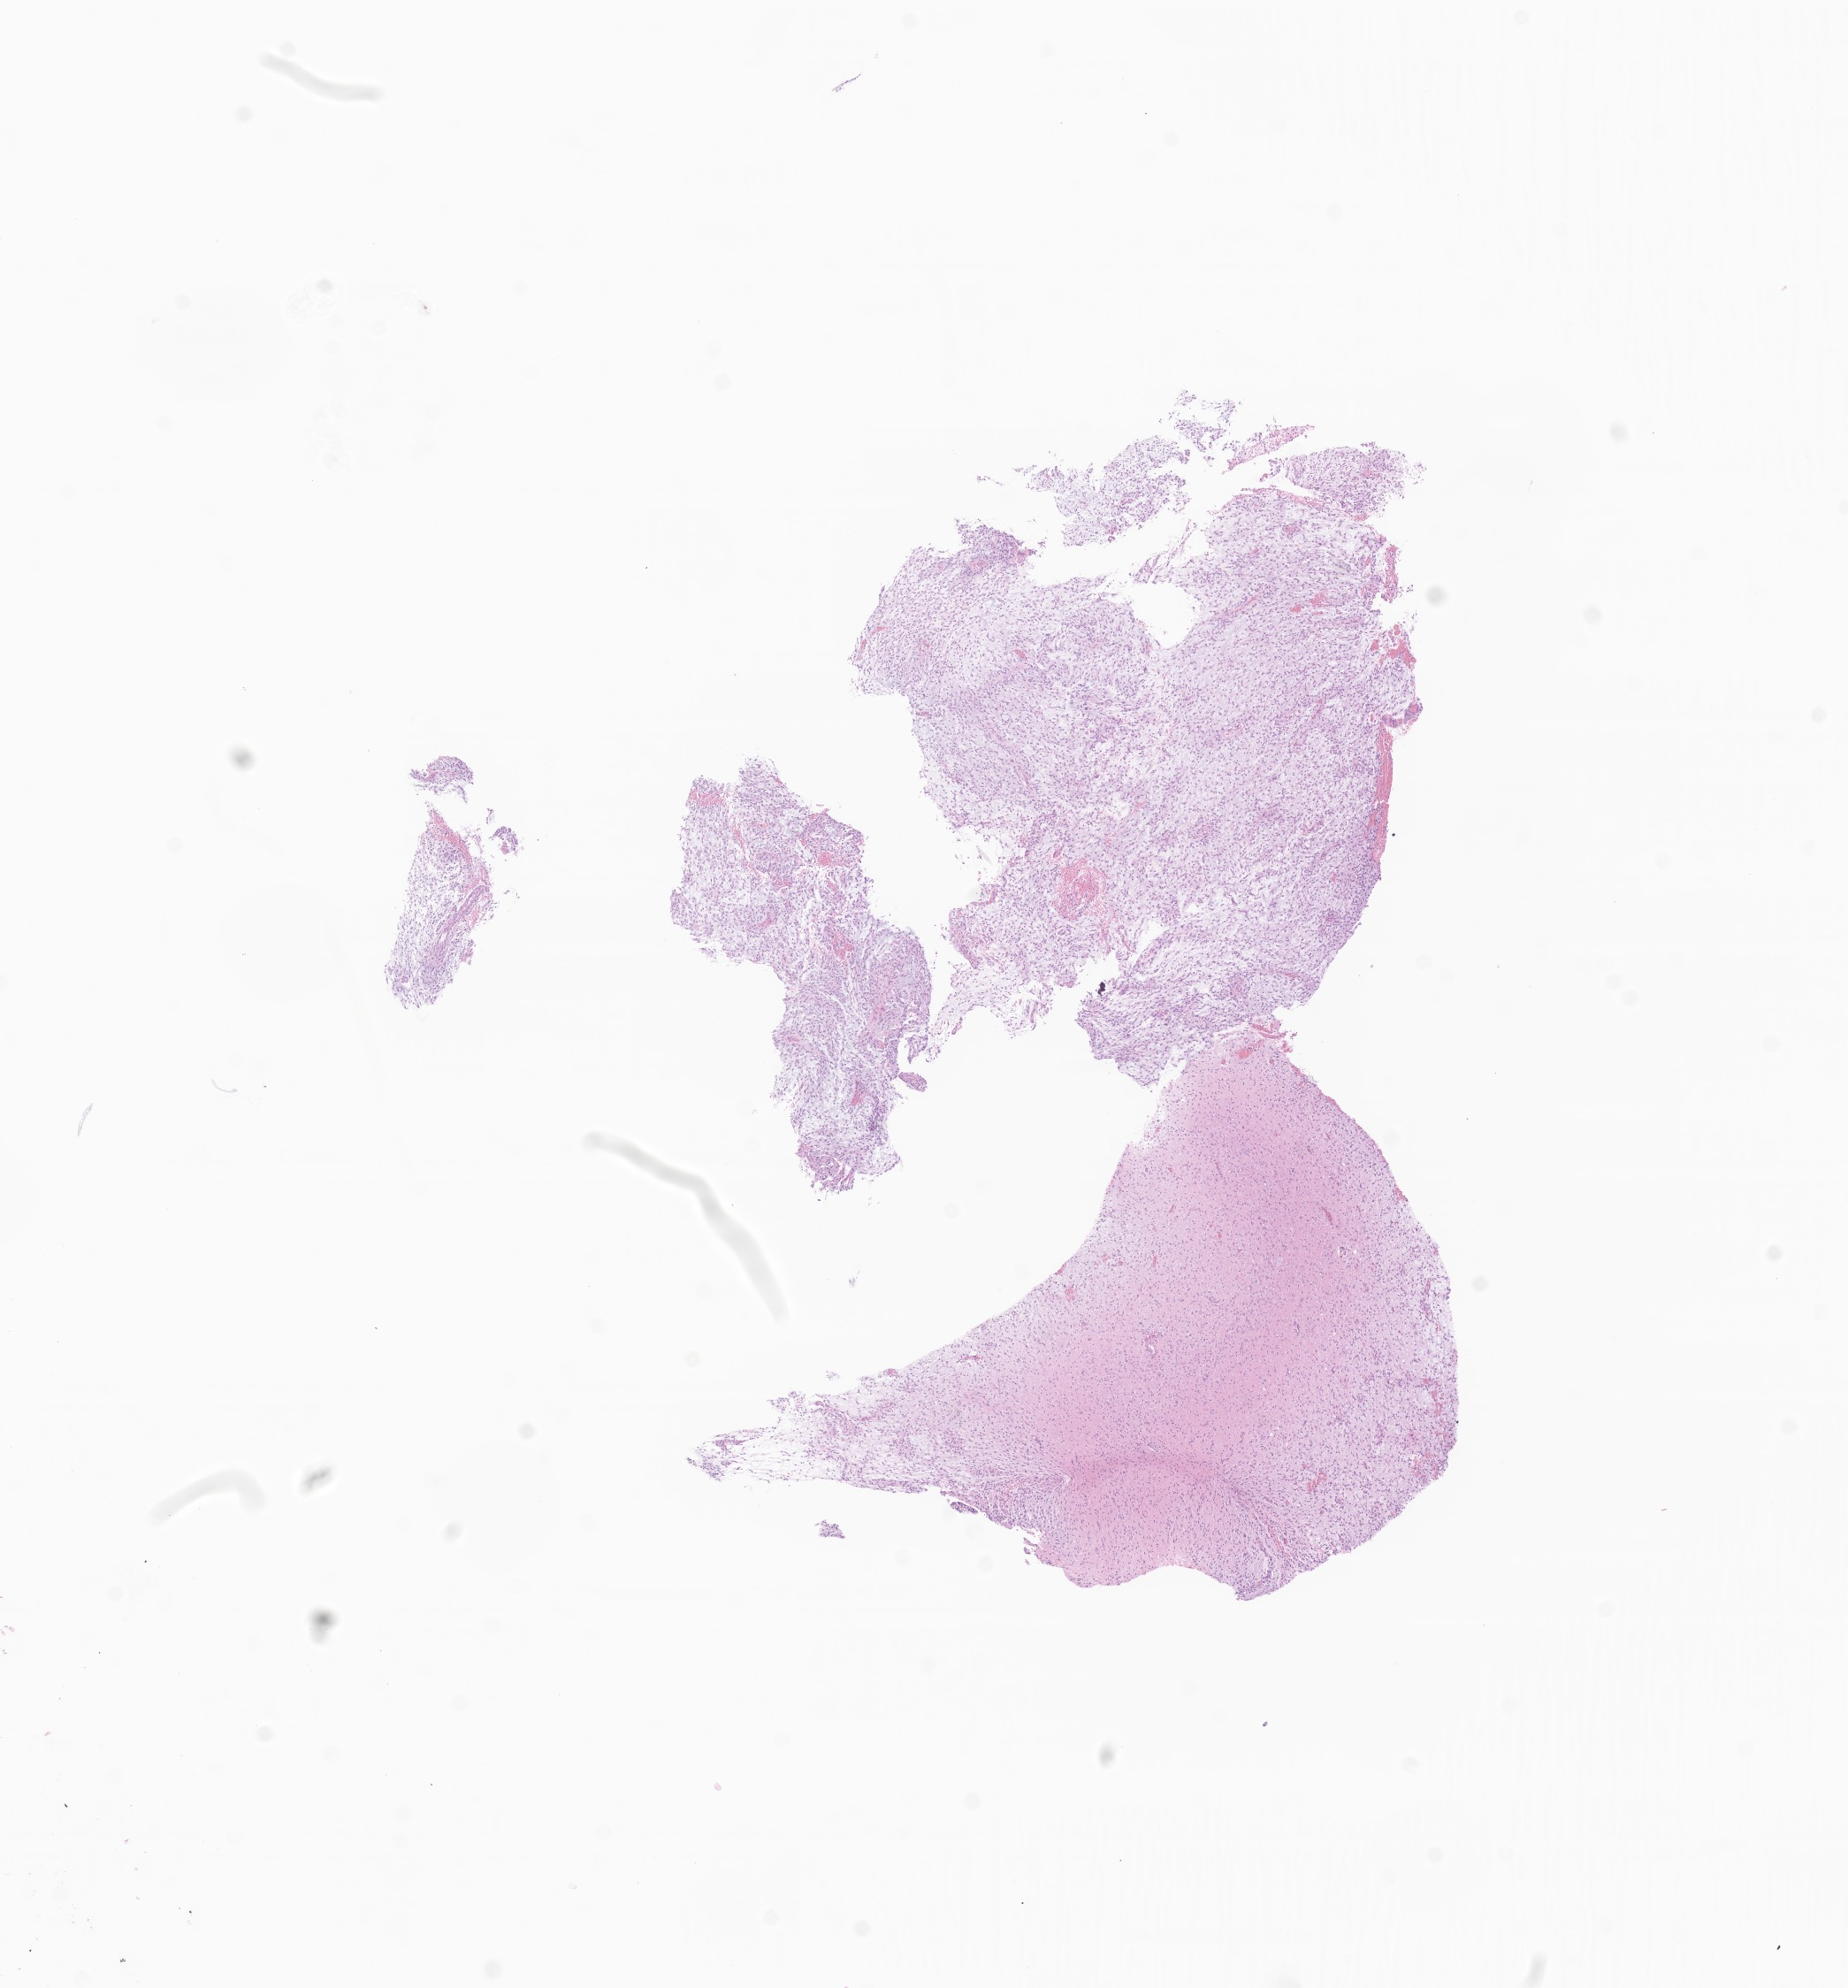
Digitized haematoxylin and eosin-stained section of tumor tissue from the brain, low-resolution overview of the scanned area, about 8.8 x 9.5 mm. FFPE section. Male patient, age 37 months (3 years 1 month).
Diagnosis: Pilocytic astrocytoma.